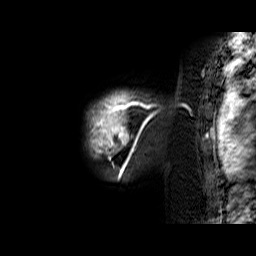
Breast MRI (dynamic contrast-enhanced), one sagittal slice. Position 55 of 60 along the scan axis. Dynamic contrast-enhanced series, time point 2 of 6 at this slice position (early post-contrast). 1.5 T. TE 6.4 ms, TR 32.9 ms. 4 mm slice thickness. 256 × 256 image matrix, field of view 200 × 200 mm. Female patient. From the clinical record (not read from this slice): setting: breast cancer imaged before/during neoadjuvant chemotherapy; receptor status: triple-negative.
Annotated regions visible in this slice (semi-automatic segmentation, software-assisted and operator-edited):
- analysis volume of interest (the breast-tissue region the enhancement analysis was run in; not a lesion): bounding box <88,91,159,174> (left, top, right, bottom; pixels)
- tumour enhancement mask (voxels above the 100 % enhancement threshold inside the analysis volume of interest): <88,91,159,174>